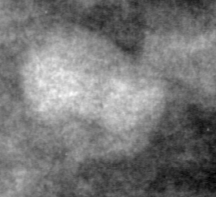
Region of interest cut from a scanned film mammogram (one marked finding), right breast, CC view.
Finding: mass, shape lobulated, margins circumscribed; BI-RADS assessment category 4; pathology (as recorded): benign.